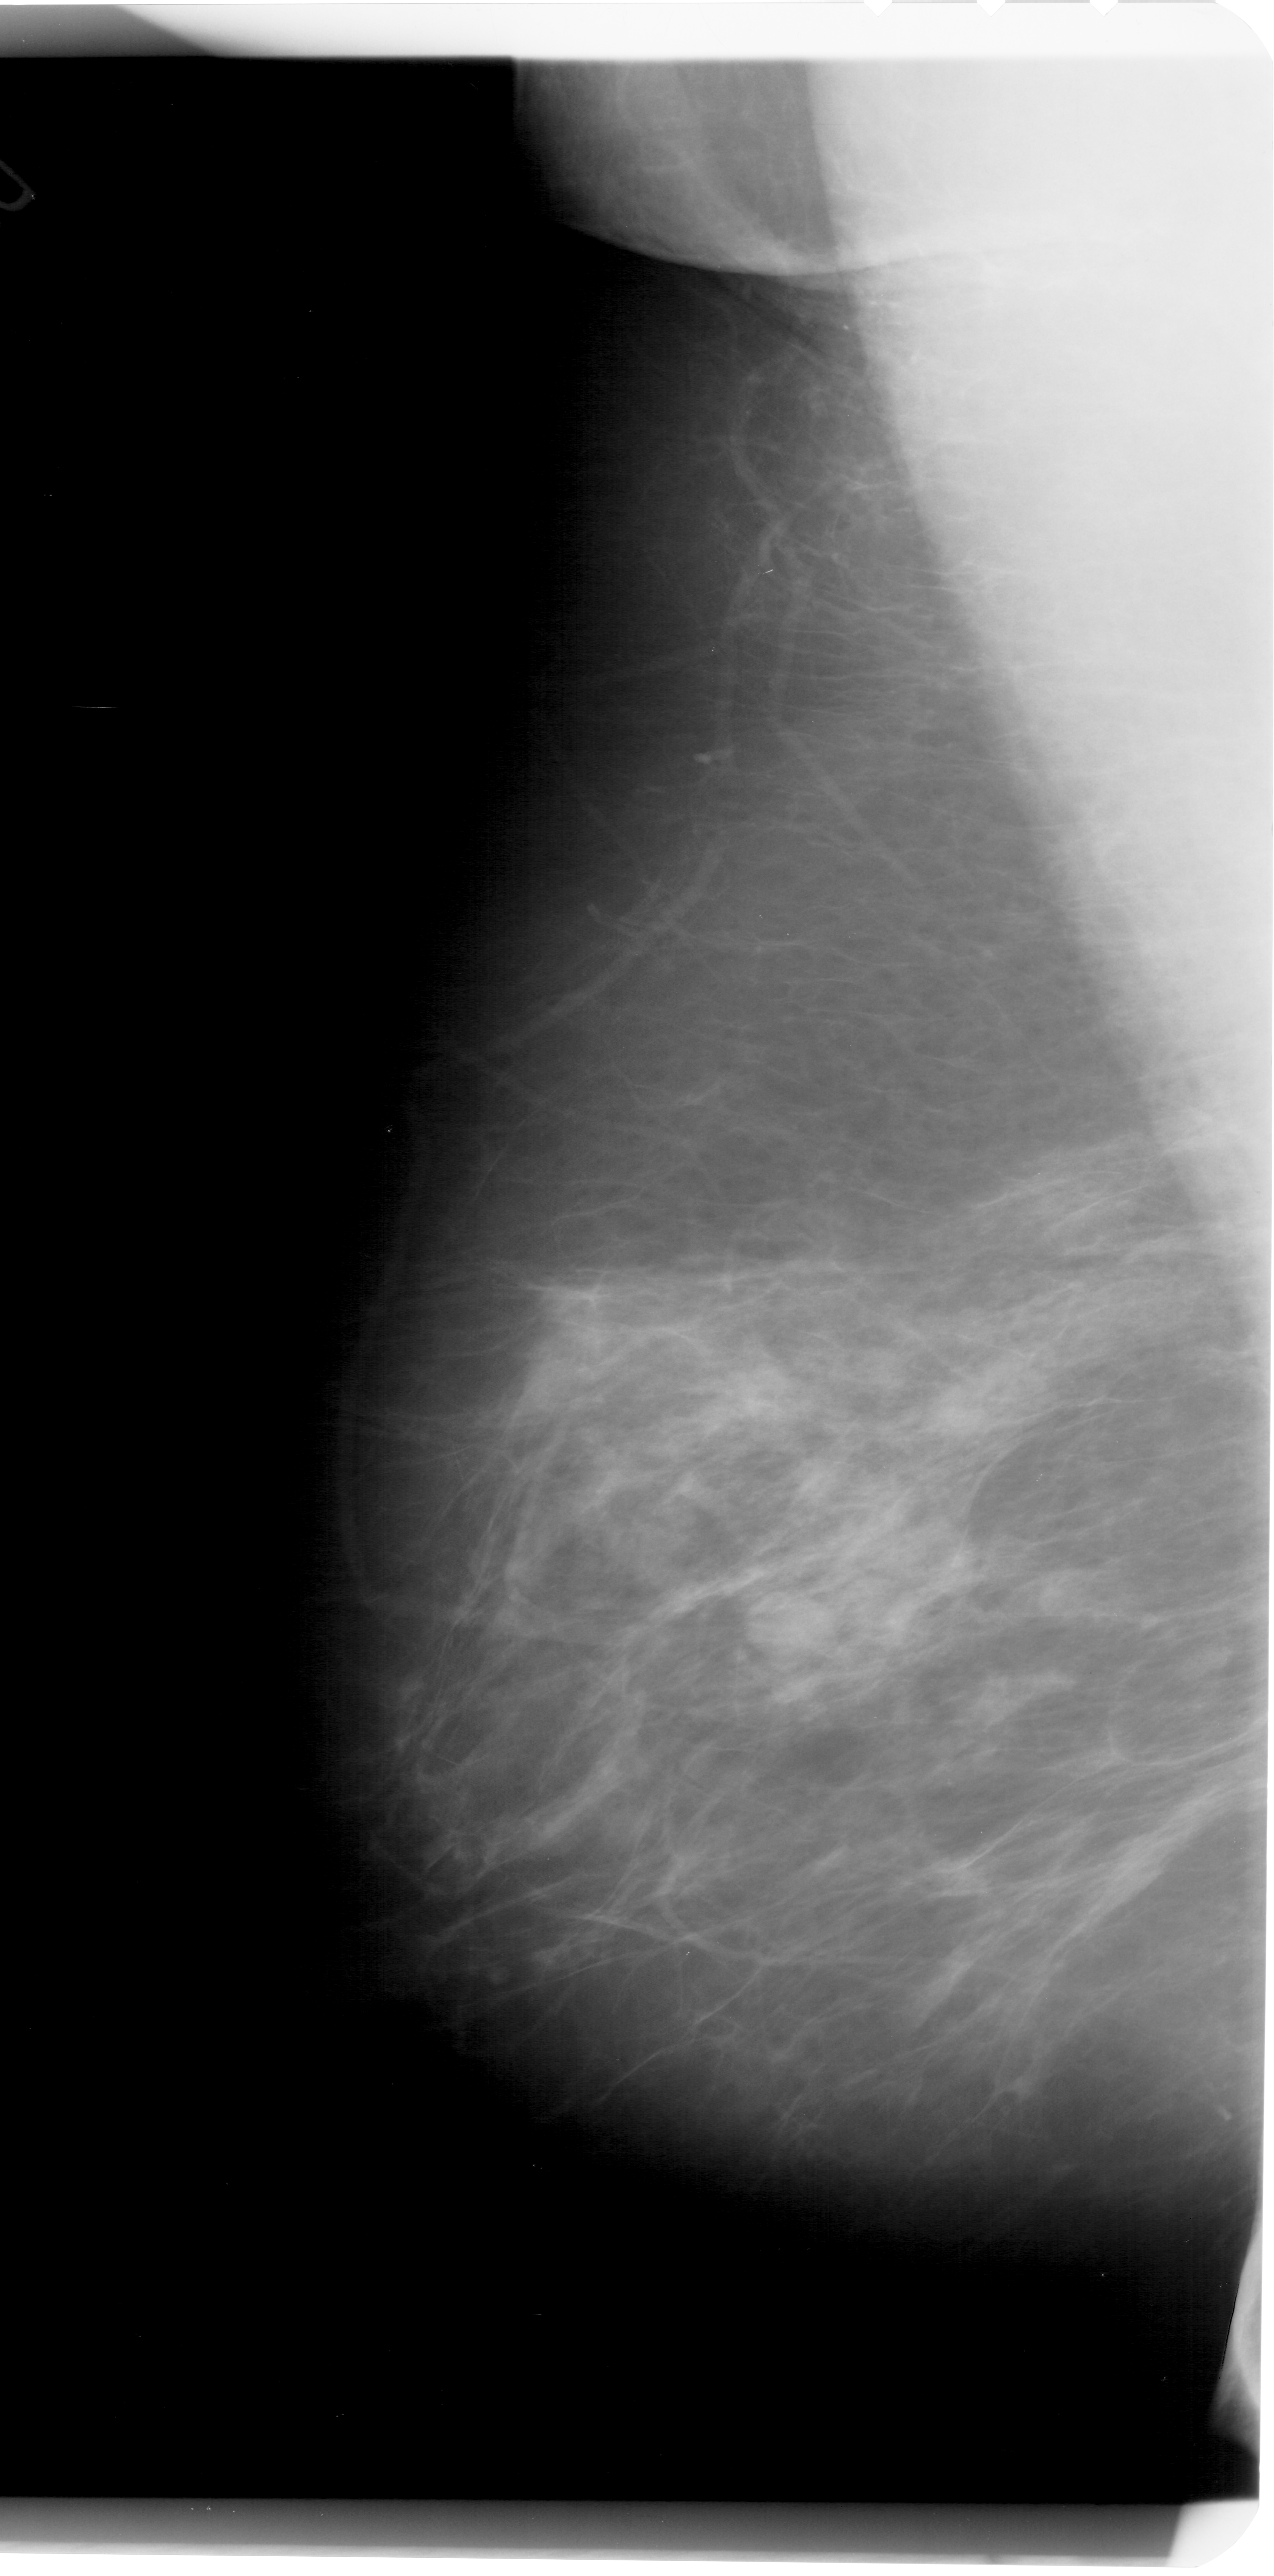
Mammogram (digitized film); left breast; MLO view; BI-RADS breast density category 2 (scale 1–4).
- Radiologist-marked abnormalities on this image: mass, shape oval, margins obscured; BI-RADS assessment category 3; subtlety rating 3 on a 1 (subtle) to 5 (obvious) scale; pathology result (as recorded, not read from the image): benign.